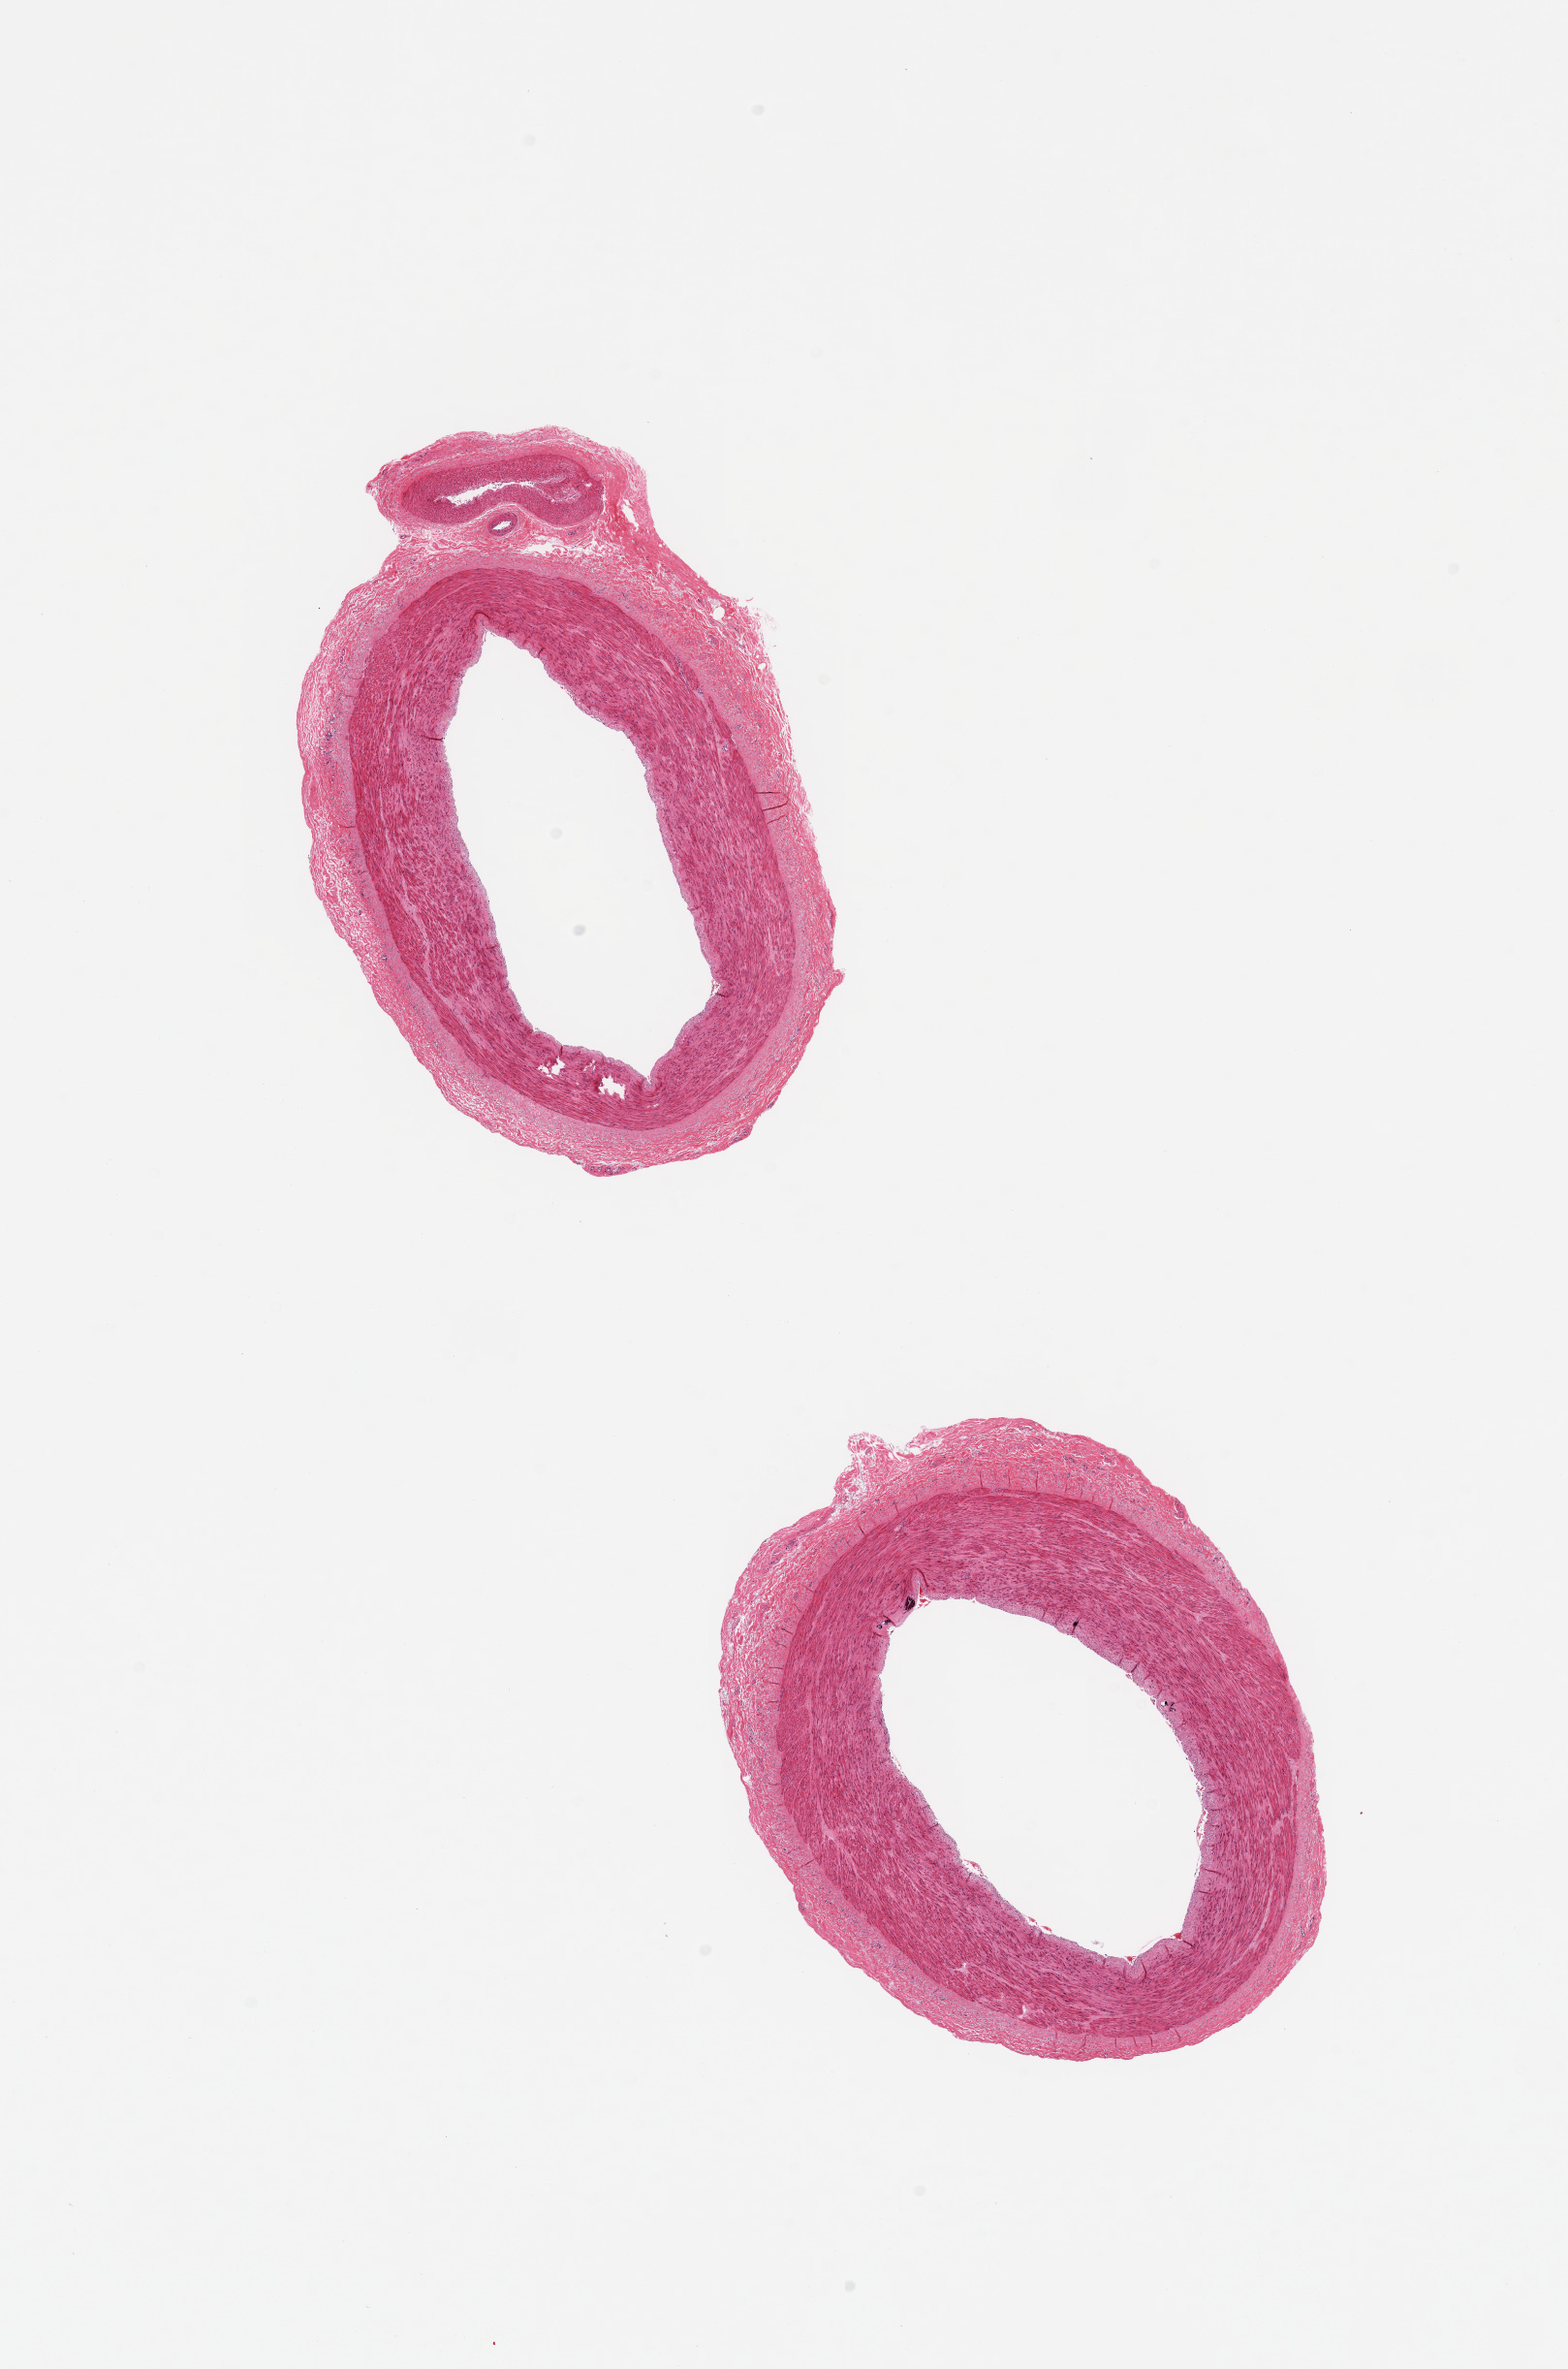
Whole-slide image, hematoxylin and eosin (H&E) stain, brightfield — low-resolution overview of the scanned area, about 12.8 x 19.3 mm. PAXgene-fixed paraffin-embedded (PFPE) section. Target tissue: tibial artery. Donor tissue sample. Male donor.
• pathologist's review note for this sample: 2 pieces; over 1mm attached adventitia with vessels